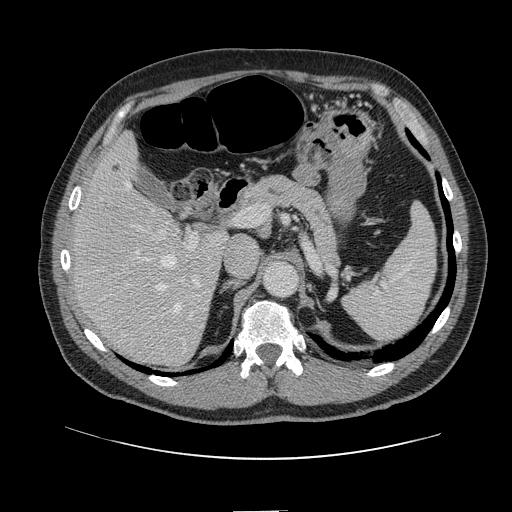
Contrast-enhanced abdominal CT, one axial slice; slice 84 of 161 in the series (ordered by position); 120 kVp; intravenous contrast given; soft-tissue window (W 400 / L 40 HU); 2.5 mm slice thickness; 512 × 512 image matrix. Male patient, age 66 years. Case-level facts recorded for this patient, not image findings: diagnosis: colorectal cancer liver metastases, imaged before liver resection; multiple liver metastases: no; largest metastasis: 3.5 cm; disease in both lobes: no.
Structures marked on this image (outlined manually by an expert reader):
- hepatic veins: box from (x=101, y=181) to (x=184, y=313) px
- liver: (x=75, y=136)–(x=224, y=365)
- planned liver remnant (the part of the liver to remain after resection): (x=75, y=136)–(x=176, y=302)
- portal vein (with intrahepatic branches): (x=131, y=213)–(x=251, y=314)
- liver metastasis: (x=112, y=165)–(x=122, y=173)